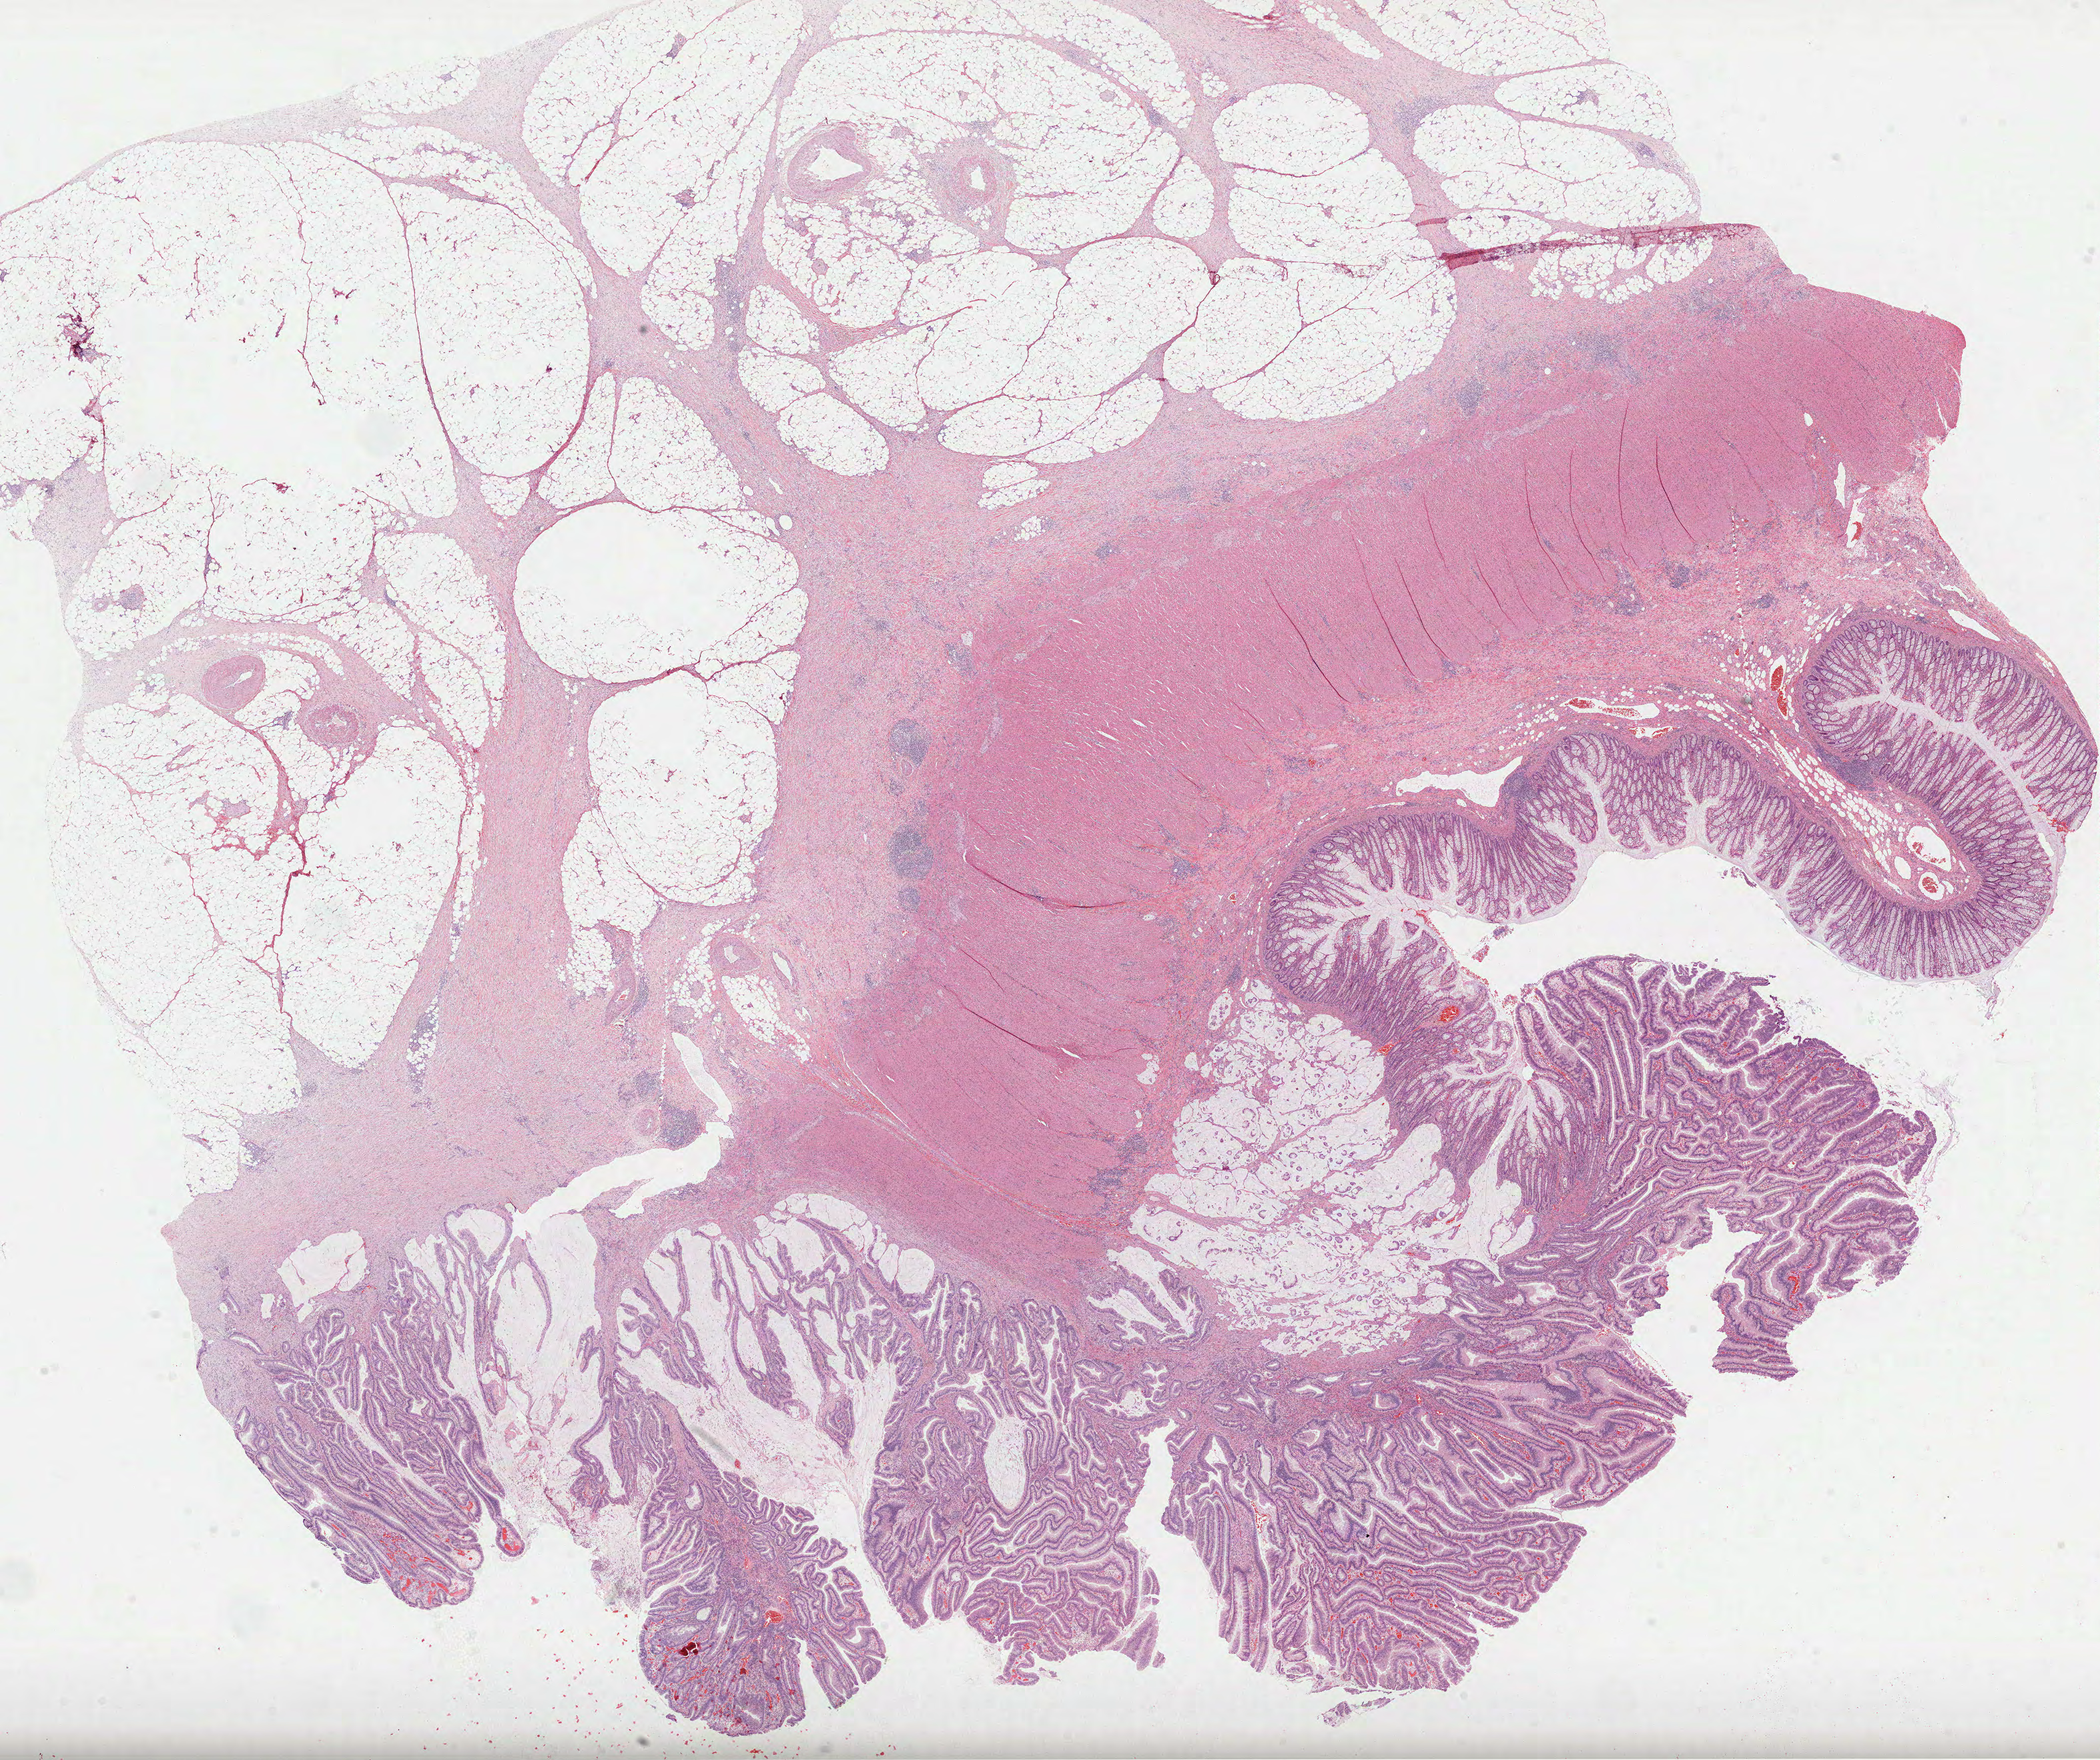
Digitized Hematoxylin and eosin (H&E) stained tissue section (whole slide), a low-resolution overview of the entire scanned area, about 25.4 x 21.3 mm. Formalin-fixed paraffin-embedded (FFPE) diagnostic section. Sample: primary tumour, colon. Patient: male, age at initial diagnosis 65 years.
TNM: T3 N1 MX. AJCC pathologic stage: IIIB (6th edition). Pathologic diagnosis: Mucinous adenocarcinoma (descending colon). Lymph nodes positive (case pathology): 2 of 26 examined.